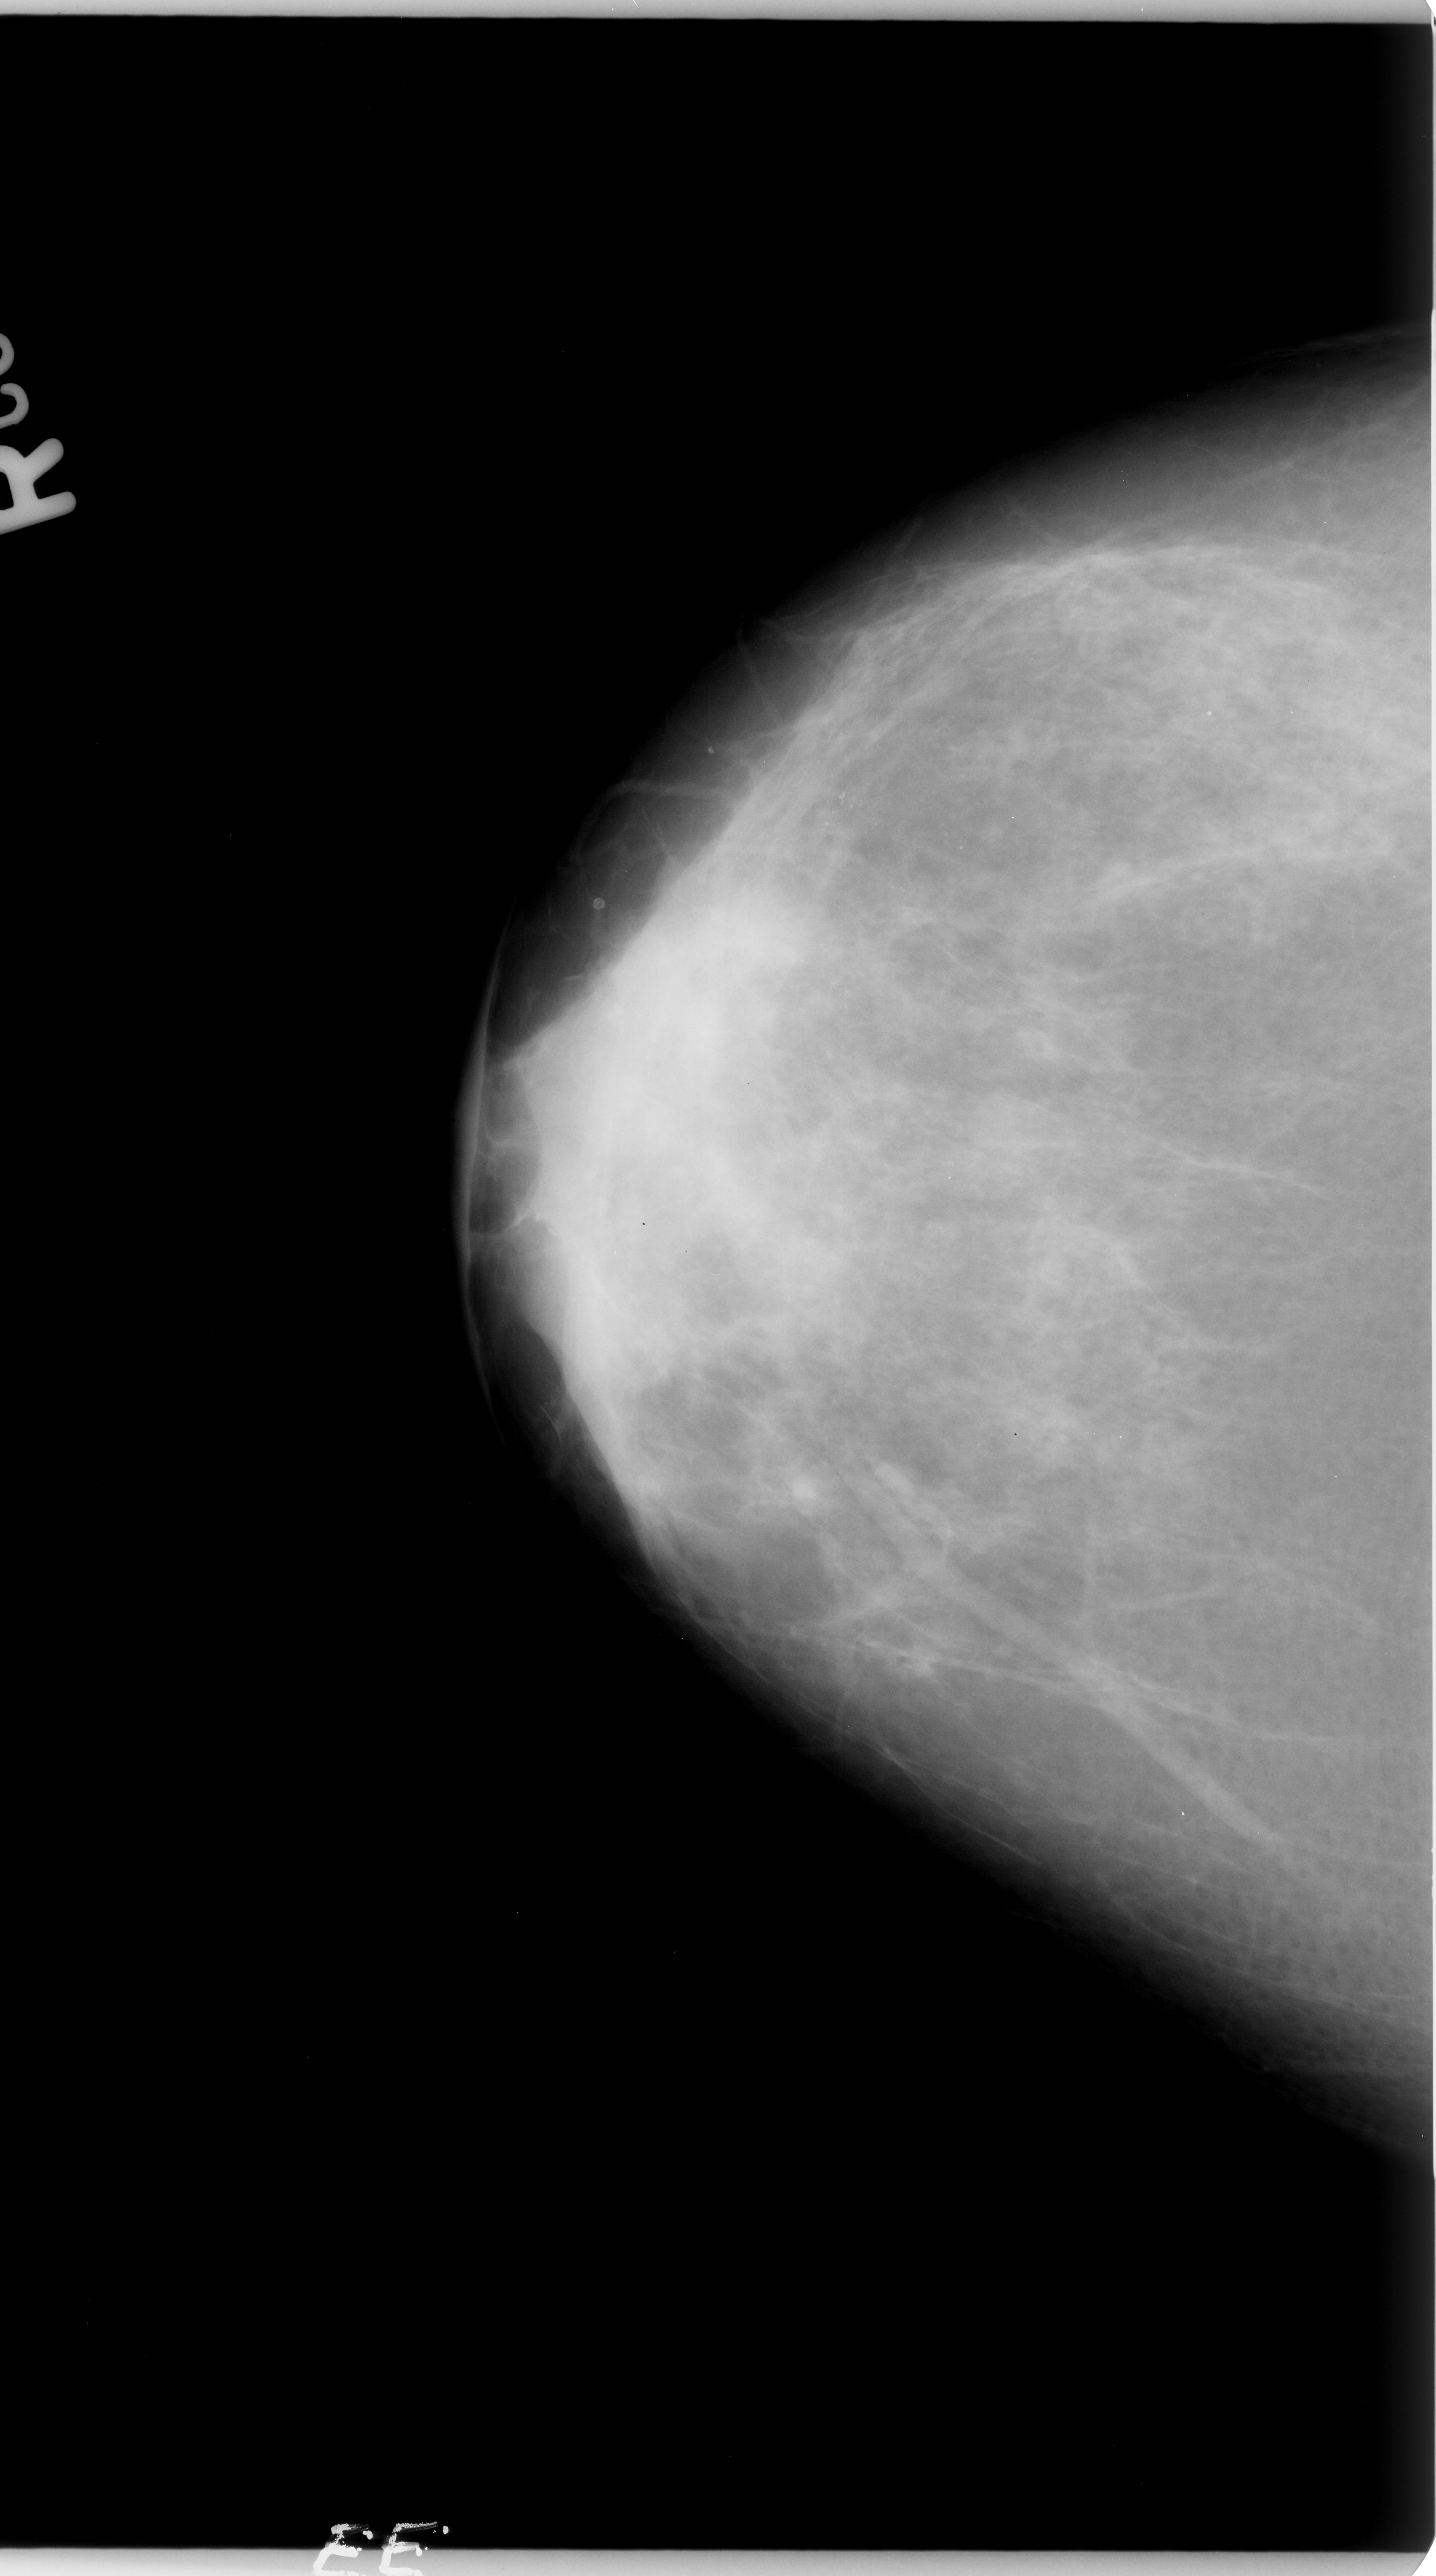
Digitized screen-film mammogram, right breast, craniocaudal (CC) view, BI-RADS breast density category 3 (scale 1–4).
Finding: calcifications, morphology pleomorphic, distribution segmental; BI-RADS assessment category 4; pathology (as recorded): benign.